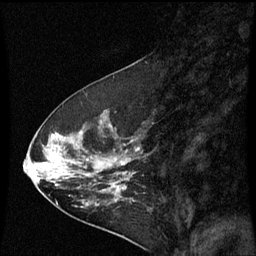
Breast MRI (dynamic contrast-enhanced), one sagittal slice; position 25 of 60 along the scan axis; dynamic contrast-enhanced series, image 2 of 3 at this slice position (ordered by acquisition); 1.5 T; TE 4.2 ms, TR 8.9 ms; 2 mm slice thickness; 256 × 256 image matrix, field of view 200 × 200 mm. Patient: female, 53 years. Case-level facts recorded for this patient, not image findings: setting: breast cancer imaged before/during neoadjuvant chemotherapy; receptor status: HR-positive, HER2-negative.
Outlined on this slice (semi-automatic segmentation, software-assisted and operator-edited):
- analysis volume of interest (the breast-tissue region the enhancement analysis was run in; not a lesion): bounding box <32,100,145,221> (left, top, right, bottom; pixels)
- tumour enhancement mask (voxels above the 70 % enhancement threshold inside the analysis volume of interest): <52,134,127,205>